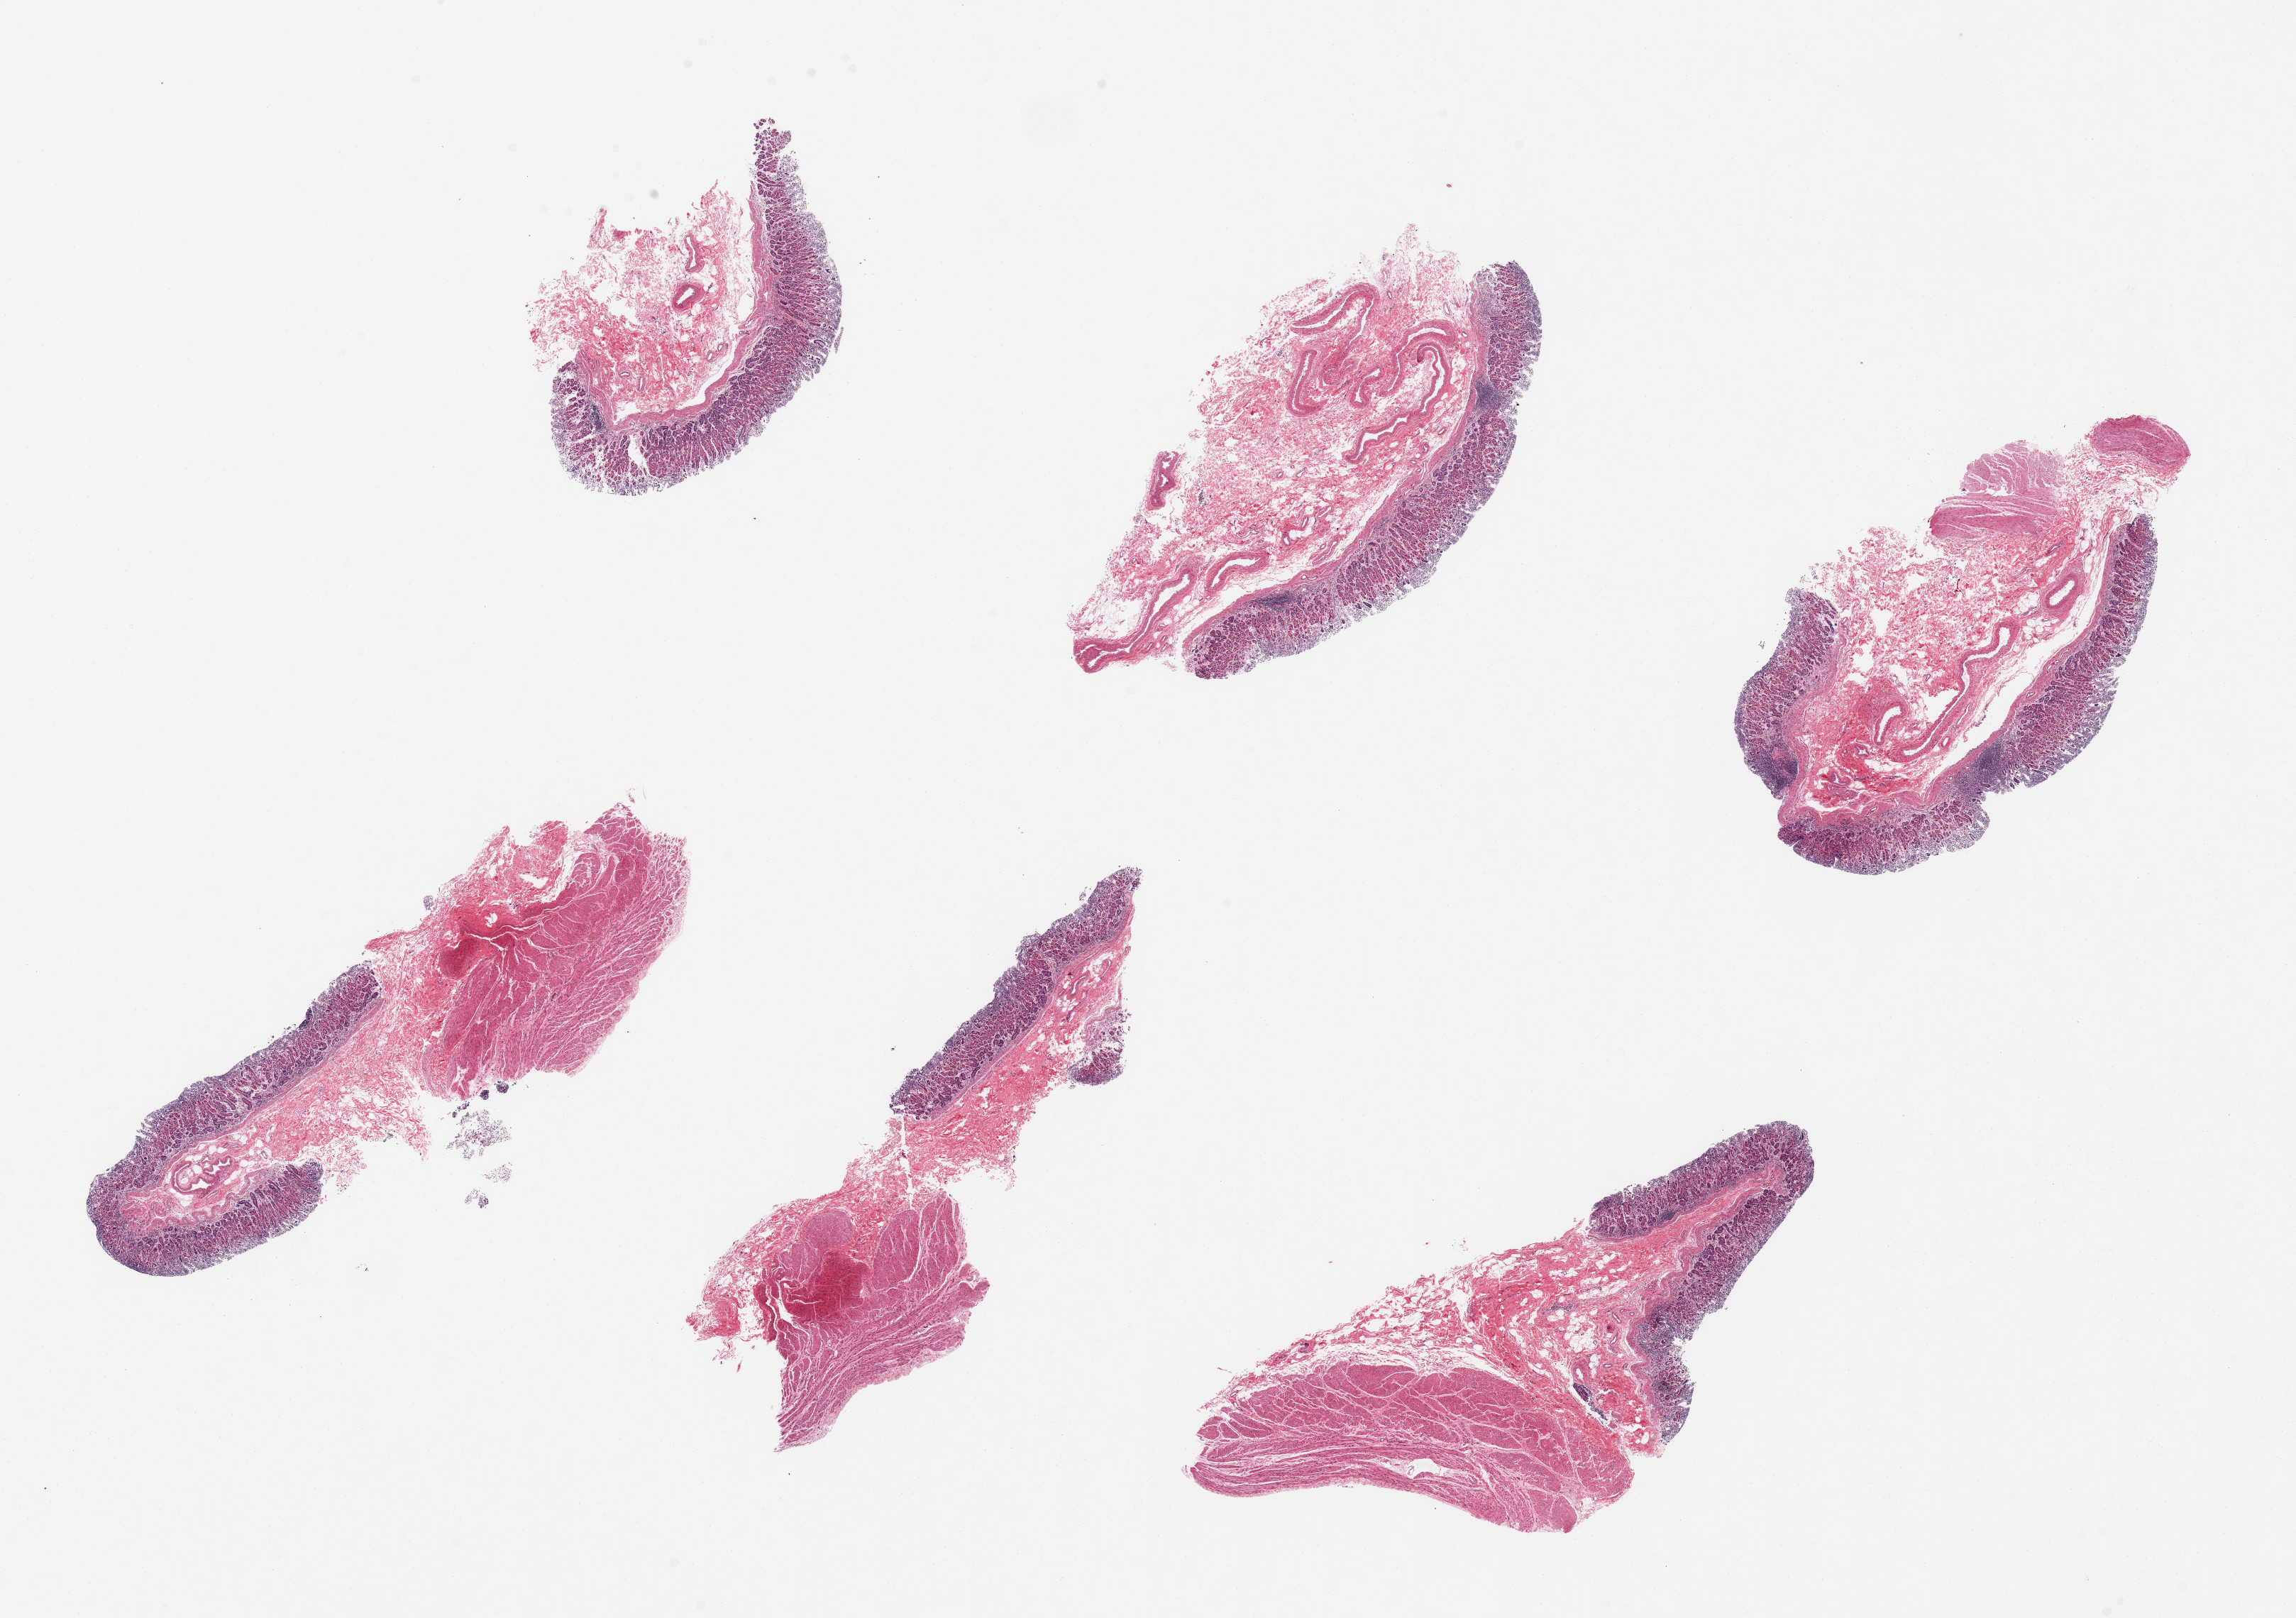
Digitized haematoxylin and eosin-stained section, brightfield — a low-resolution overview of the entire scanned area, about 25.6 x 18.0 mm, PAXgene-fixed paraffin-embedded (PFPE) section, sampled site (target tissue): stomach, tissue donor sample.
Pathologist's review note for this sample: 6 pieces; chronic inflammatory cells in the superficial lamina propria.